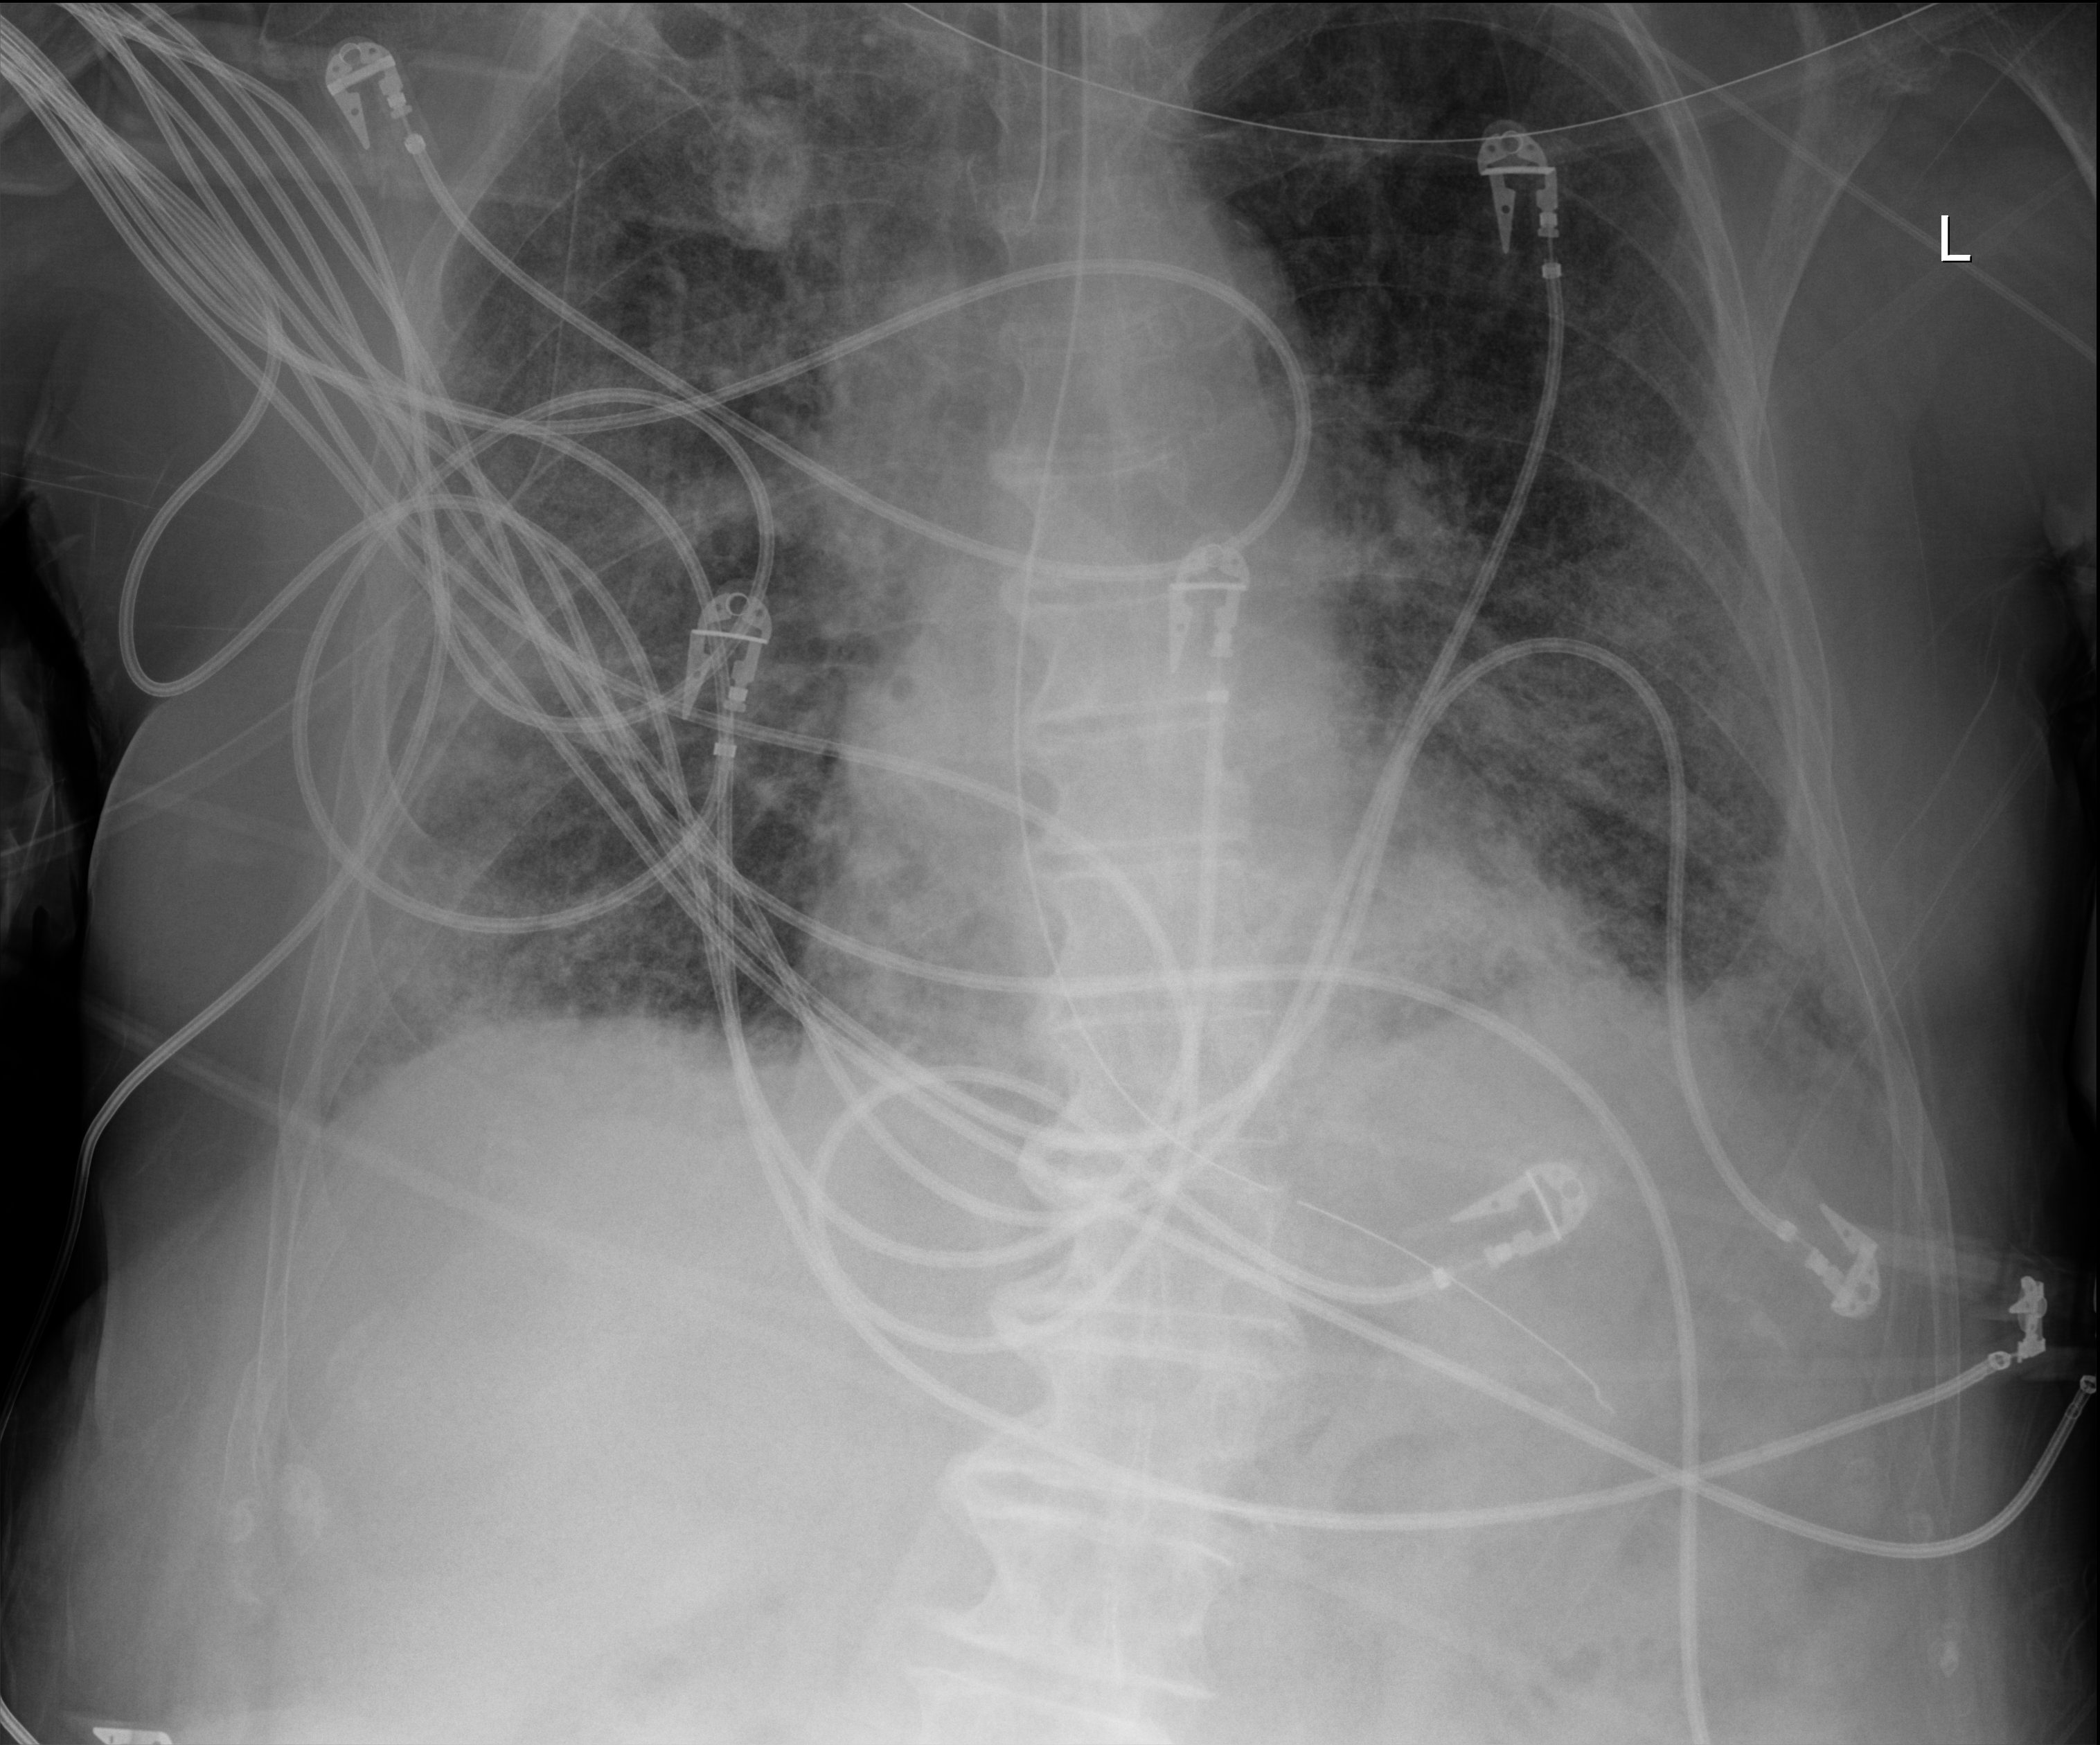
Bedside chest radiograph (digital radiography); anteroposterior (AP) projection. Patient hospitalised with COVID-19; male, aged 75–90 years.
Admission-level facts for this patient (not findings on this image; timing relative to this image not recorded):
- length of hospital stay: 47 days
- admitted to intensive care during this hospital stay: yes